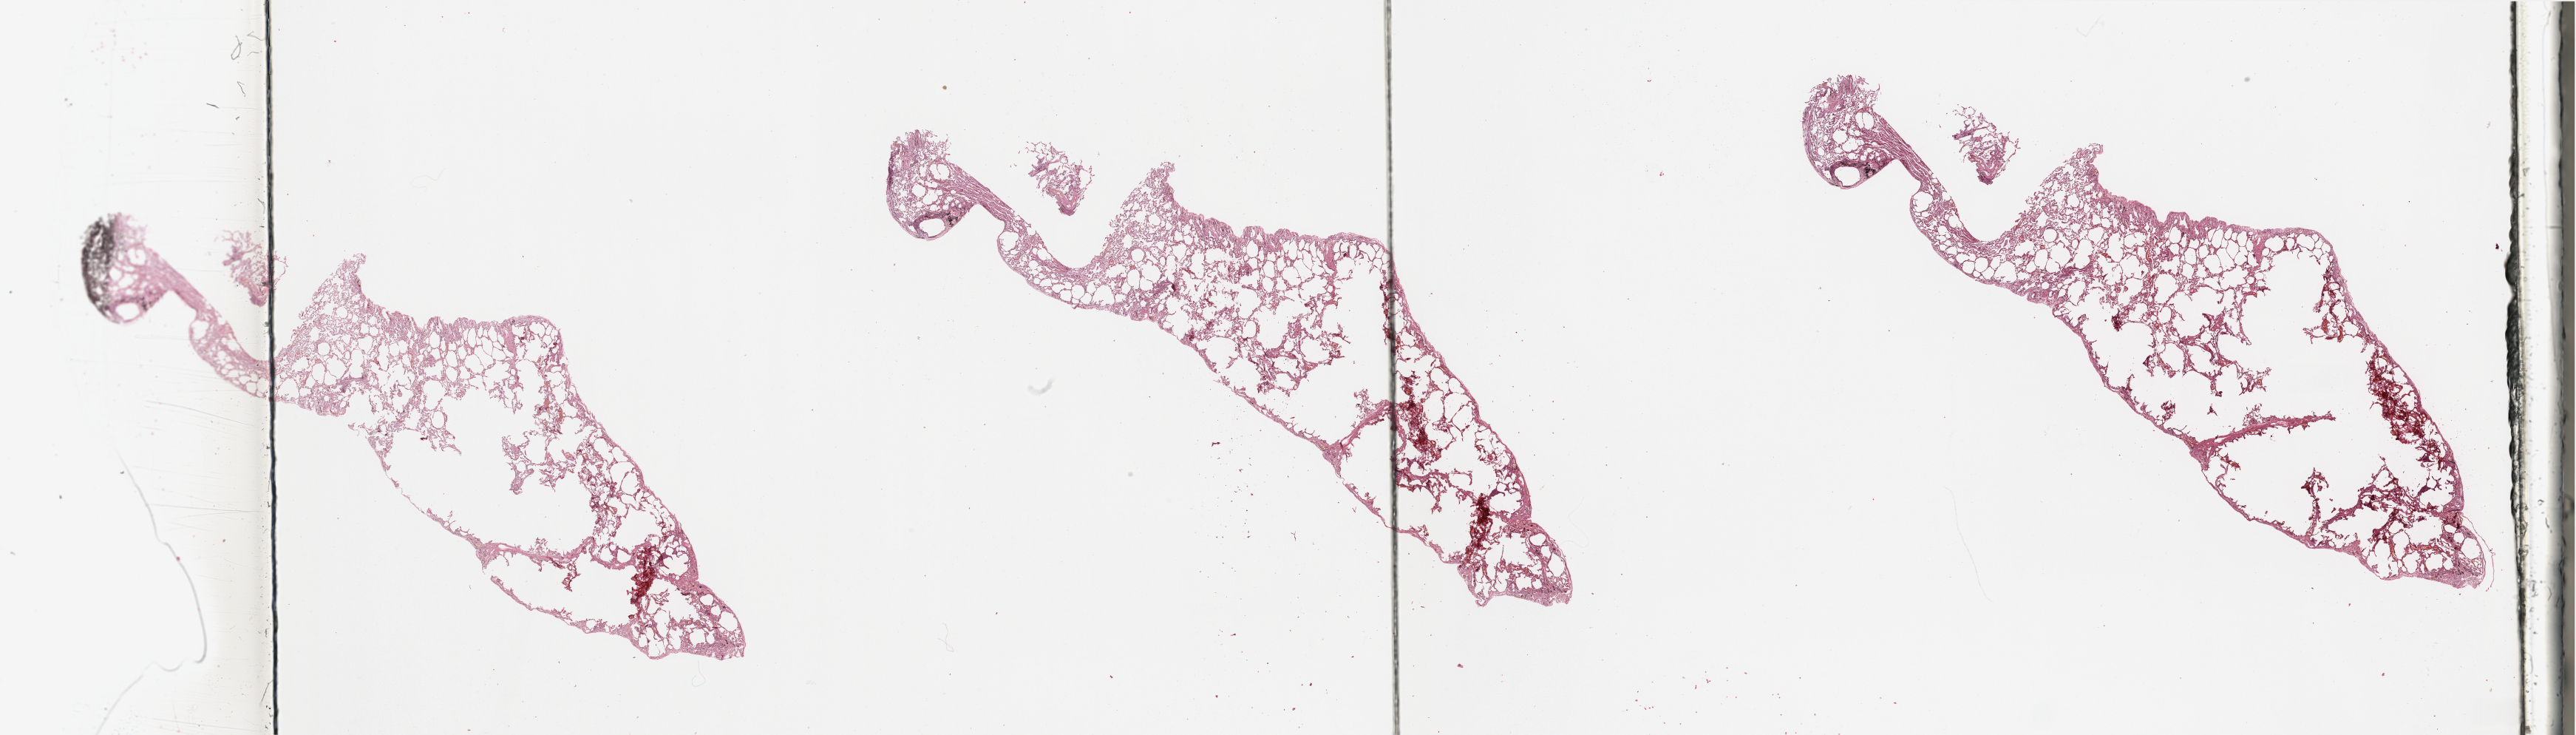
Hematoxylin and eosin (H&E) stained whole-slide image, shown as a low-resolution overview of the whole scanned area (about 55.1 x 15.7 mm, acquisition: 20x scan). Normal (non-tumour) tissue sample, sampled site: lung. 72-year-old male patient.
This section: normal (non-tumour) tissue from the same patient. Patient diagnosis: Adenocarcinoma, NOS.